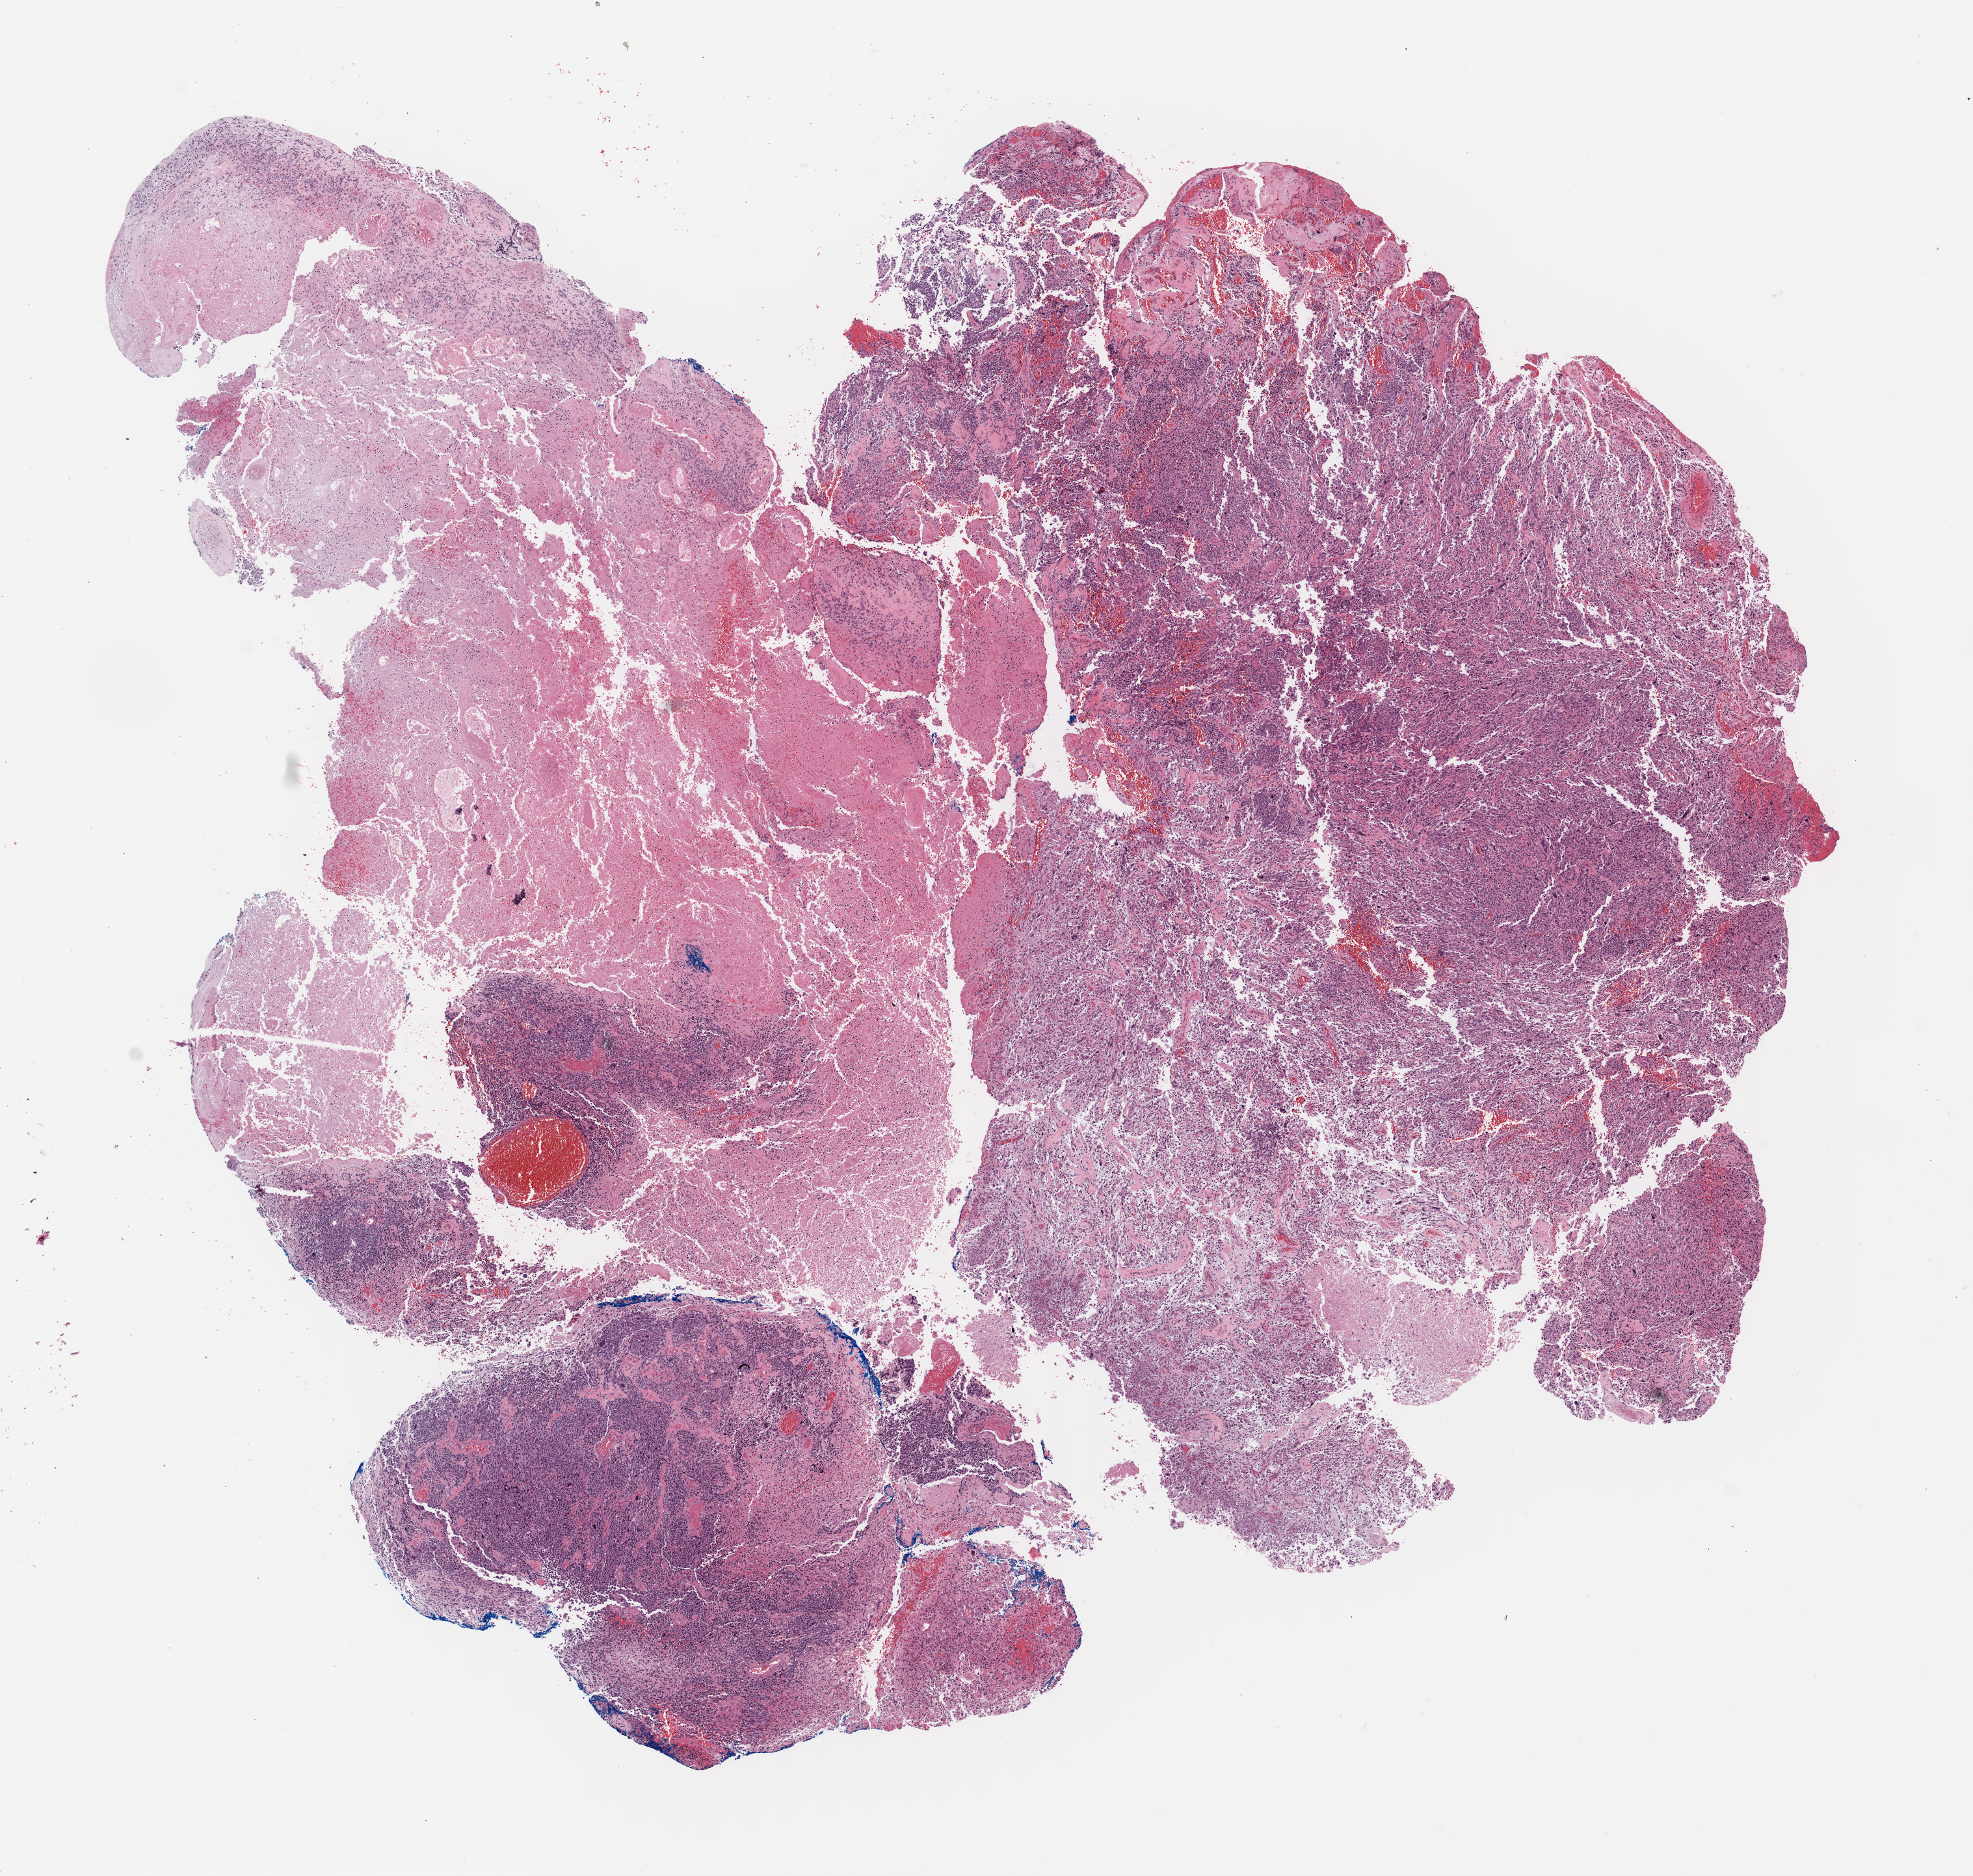
Hematoxylin and eosin (H&E) stained whole-slide image — shown as a low-resolution overview of the whole scanned area (about 11.9 x 11.3 mm, slide scanned at 40x); formalin-fixed paraffin-embedded (FFPE) diagnostic section; brain, primary tumour sample. Patient: male, age at initial diagnosis 39 years.
• diagnosis: Glioblastoma